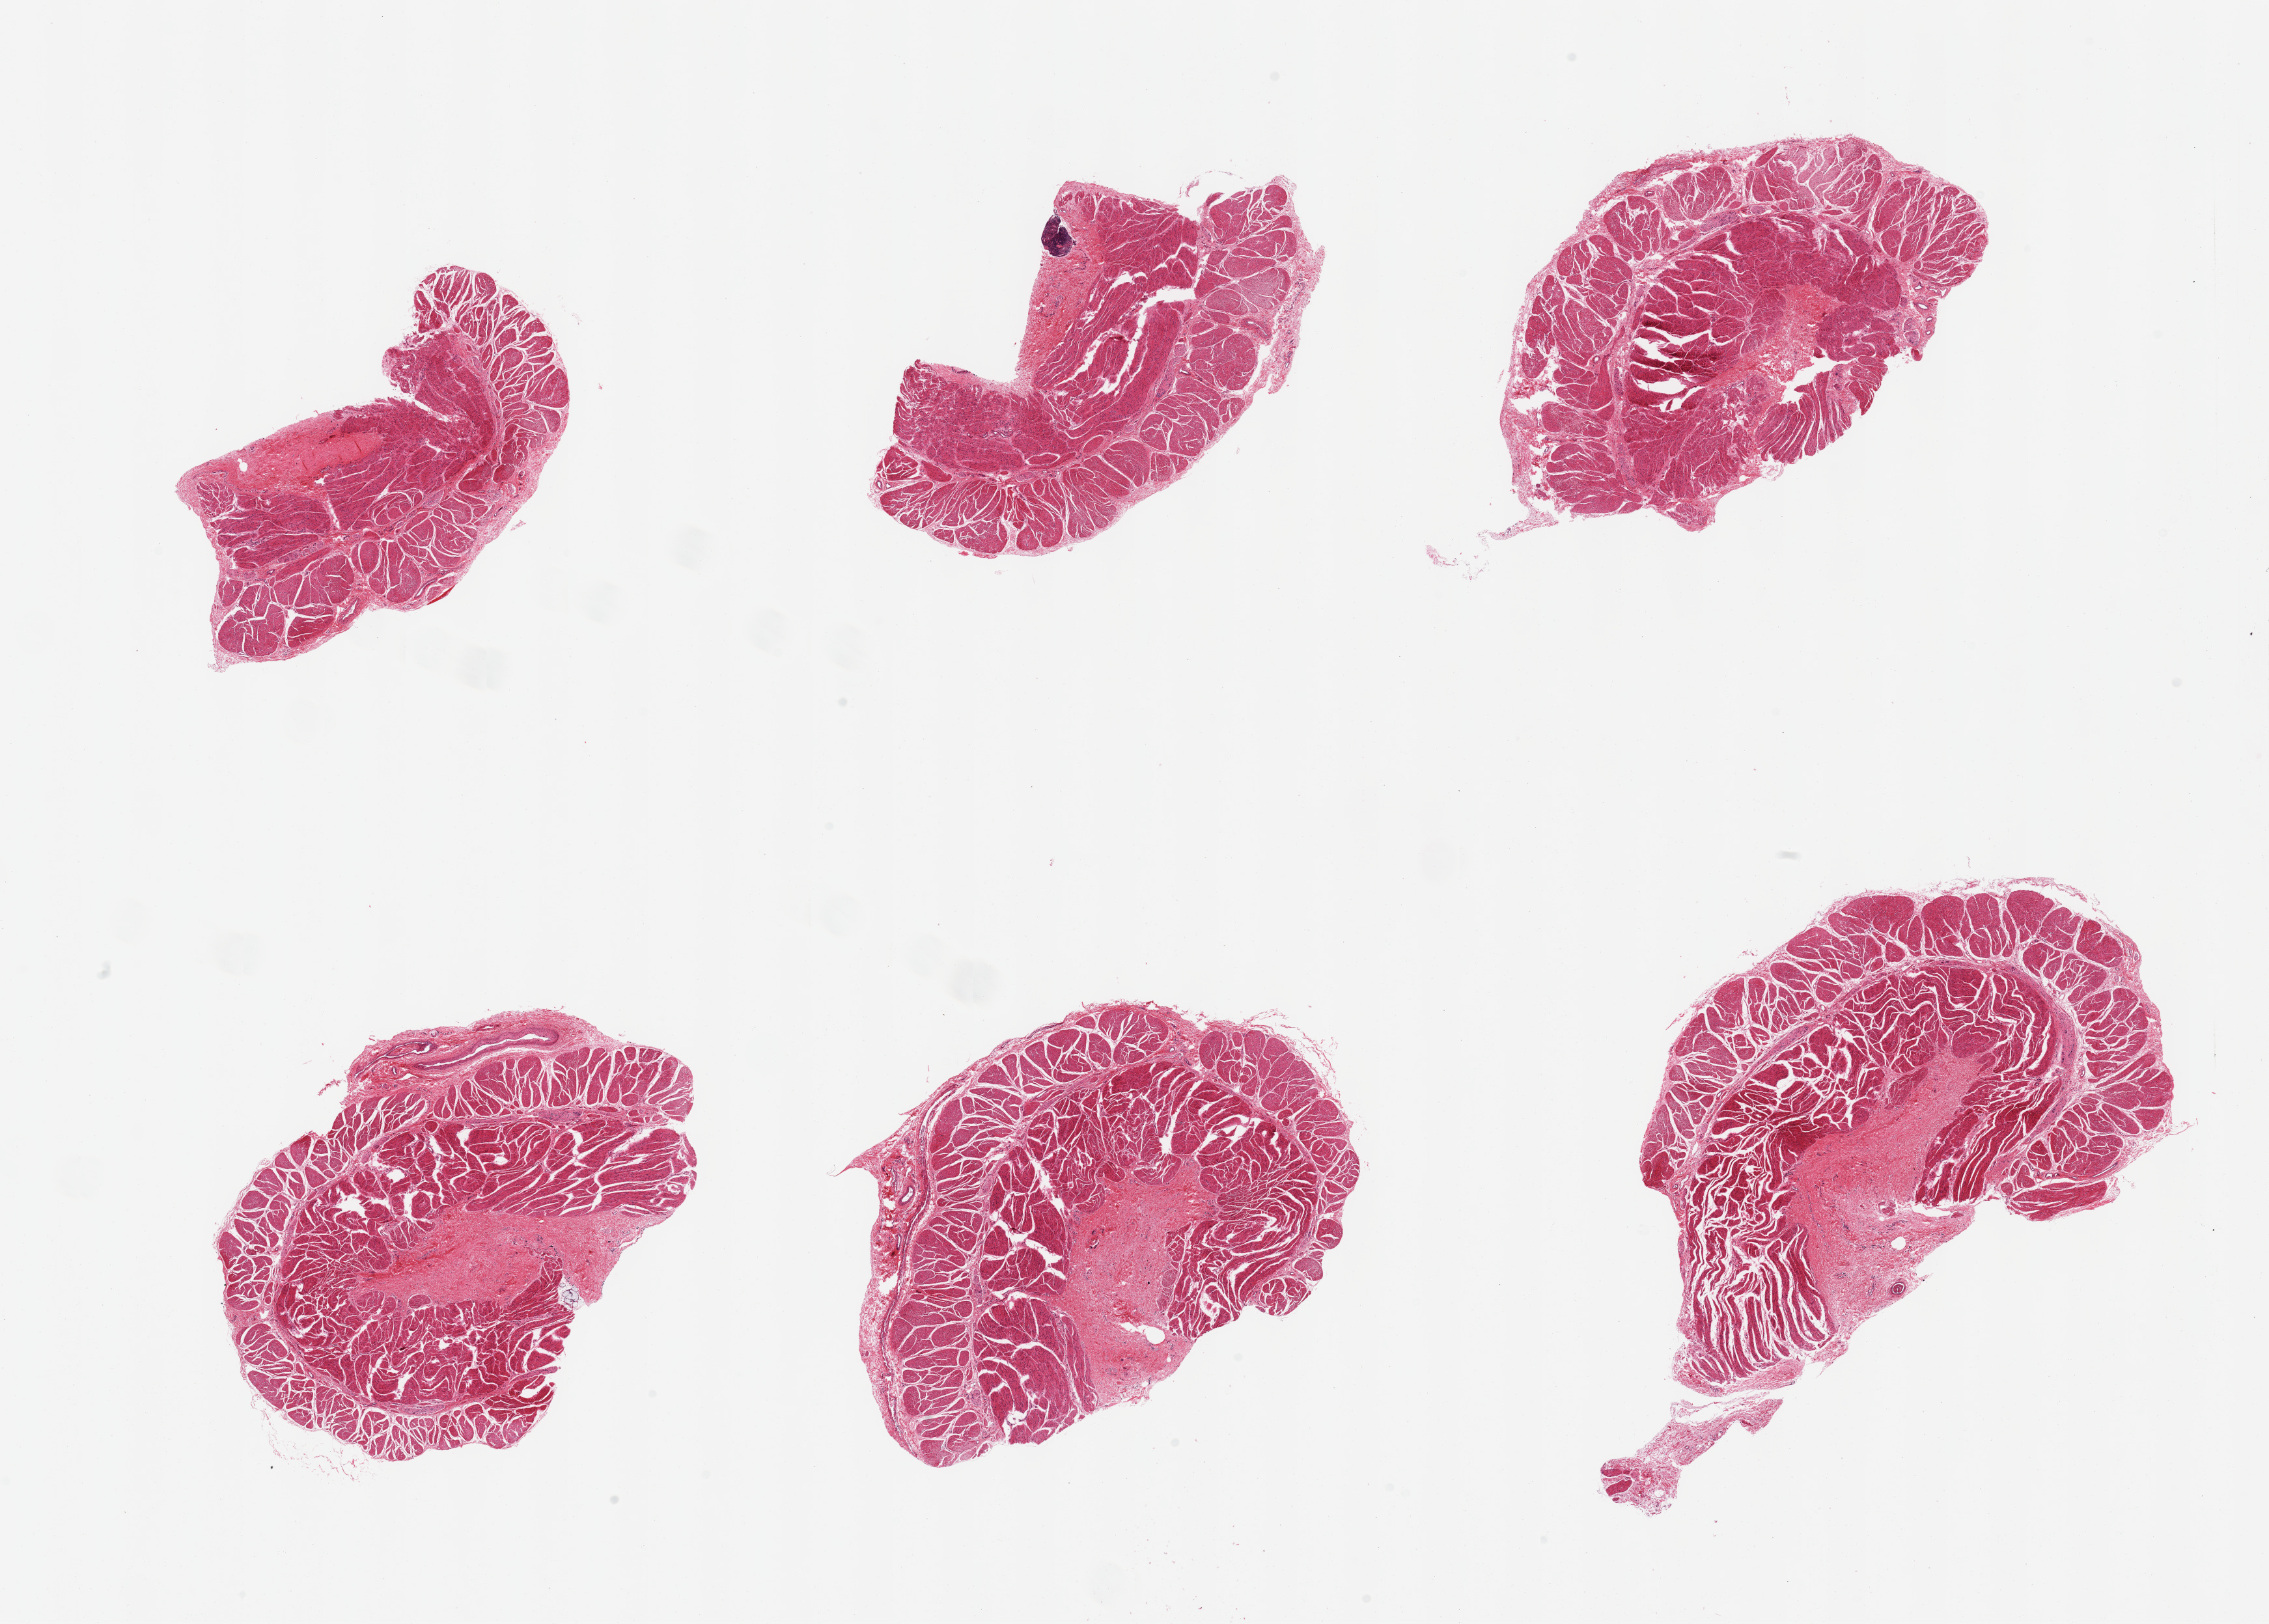
Whole-slide image, hematoxylin and eosin (H&E) stain, a low-resolution overview of the entire scanned area, about 27.6 x 19.7 mm, PAXgene-fixed, paraffin-embedded tissue, sampled site (target tissue): gastroesophageal junction, donor tissue sample. Donor sex: female.
• reviewer comment on this tissue sample: 6 pieces; core of fibrous submucosa in all, occupies up to 20%